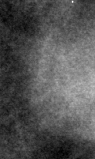
Region of interest cut from a scanned film mammogram (one marked finding), right breast, CC view, BI-RADS breast density category 2 (scale 1–4).
Finding: mass, shape round, margins circumscribed; BI-RADS assessment category 4; pathology result (as recorded, not read from the image): malignant.